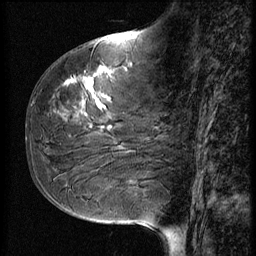
Breast MRI (dynamic contrast-enhanced), one sagittal slice; slice 25 of 56 in the series (ordered by position); 3 images stored at this slice position (order not interpretable as contrast timing); 1.5 T; TE 4.2 ms, TR 9 ms; 2.5 mm slice thickness; 256 × 256 image matrix, field of view 180 × 180 mm. Female patient, age 51 years. Case-level facts recorded for this patient, not image findings: setting: breast cancer imaged before/during neoadjuvant chemotherapy; receptor status: HR-positive, HER2-negative.
Outlined on this slice (semi-automatic segmentation, software-assisted and operator-edited):
- analysis volume of interest (the breast-tissue region the enhancement analysis was run in; not a lesion): bounding box <41,58,167,161> (left, top, right, bottom; pixels)
- tumour enhancement mask (voxels above the 140 % enhancement threshold inside the analysis volume of interest): <65,68,113,129>